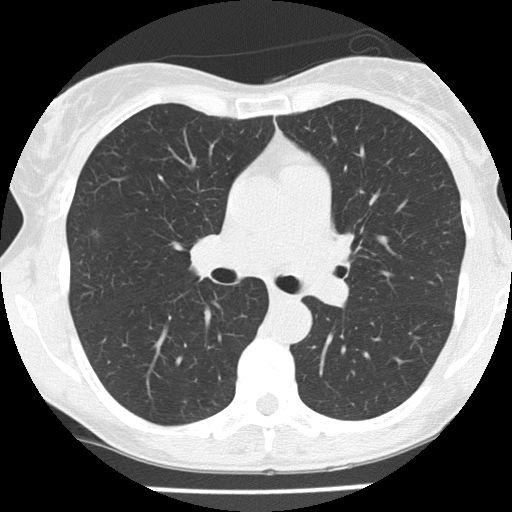
Chest CT (low-dose screening protocol), one axial image, baseline annual screen, lung window (W 1500 / L -600 HU). Female, age 56 years at enrolment. Former smoker at enrolment.
Expert reader's lesion annotation, box from (x=79, y=224) to (x=119, y=252) px. Reader record for this screening exam (exam-level; its link to the box is not recorded): non-calcified nodule or mass ≥4 mm, right upper lobe, 7 × 5 mm, poorly defined margins, ground glass attenuation. Official screen result: positive, change unspecified: nodule(s) >= 4 mm or enlarging nodule(s), mass(es), or other non-specific abnormalities suspicious for lung cancer. Later outcome: lung cancer diagnosed 148 days after this screen — bronchiolo-alveolar carcinoma, non-mucinous, right upper lobe, well differentiated (G1), stage IA (AJCC 6th edition), 6 mm at pathology.